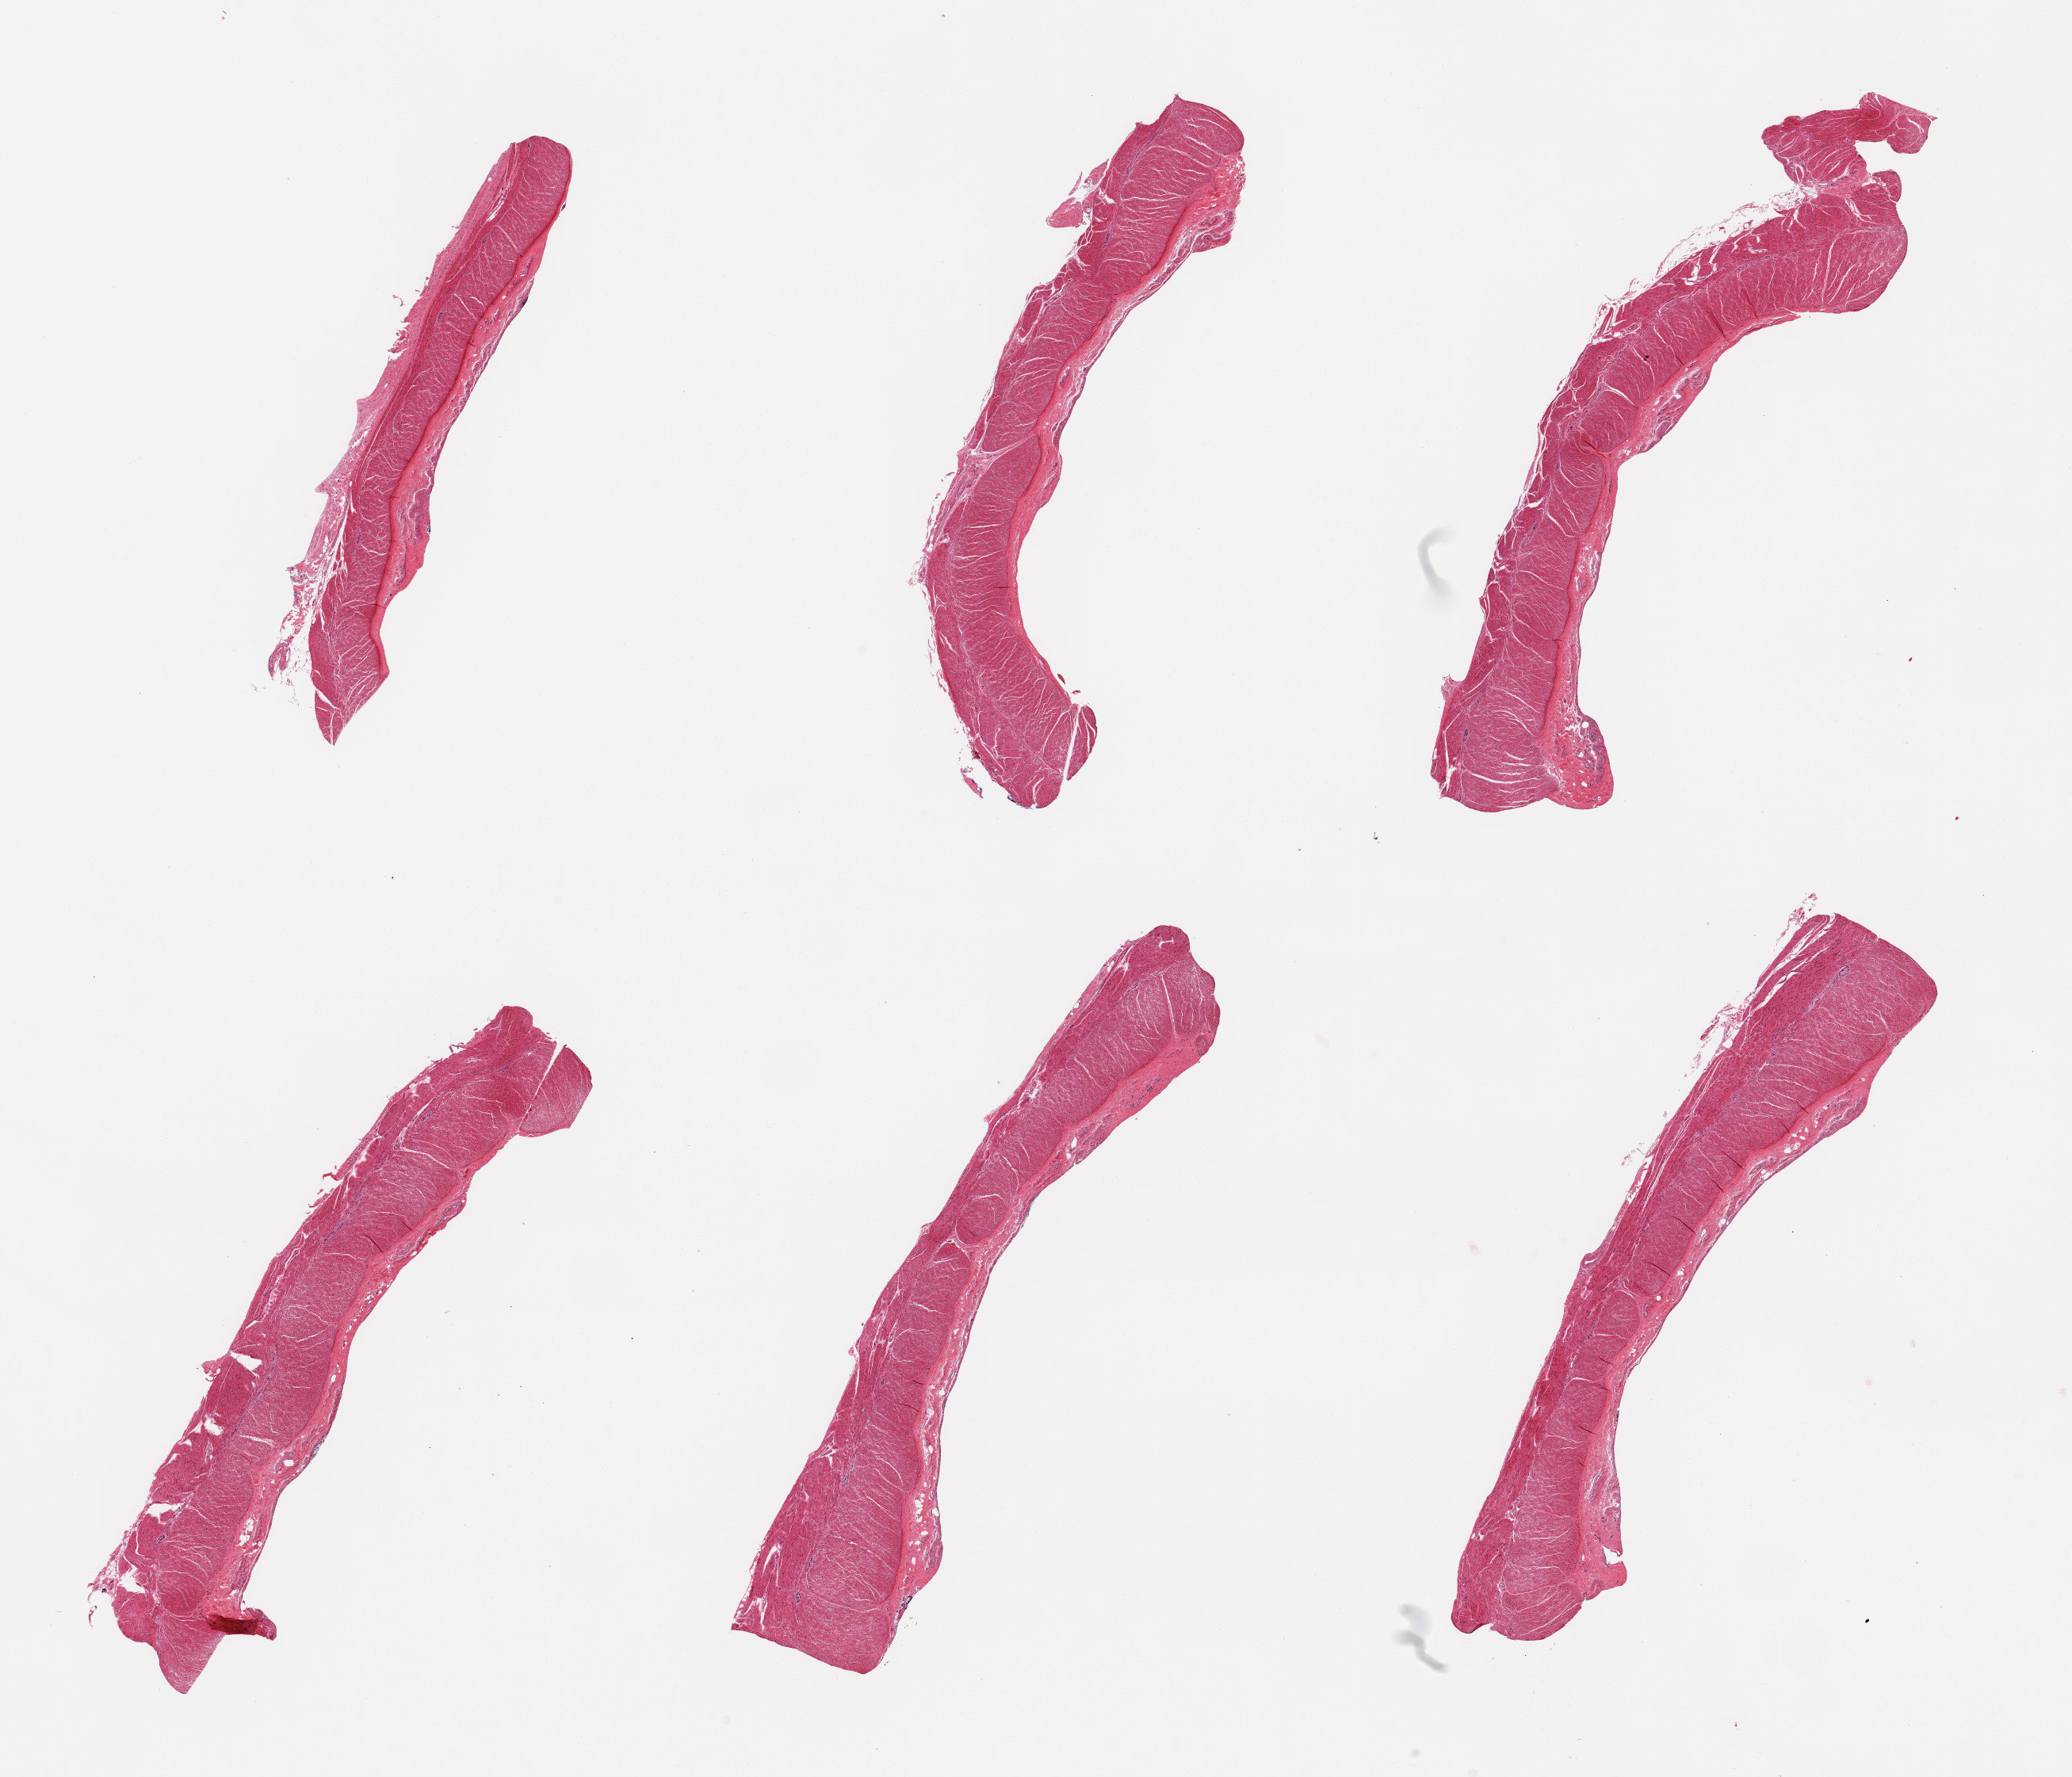
Whole-slide image, hematoxylin and eosin (H&E) stain, a low-resolution overview of the entire scanned area, about 20.7 x 17.7 mm. PAXgene-fixed, paraffin-embedded tissue. Sampled site (target tissue): sigmoid colon. Donor tissue sample. Female donor.
Reviewer comment on this tissue sample: 6 pieces; well dissected muscularis.